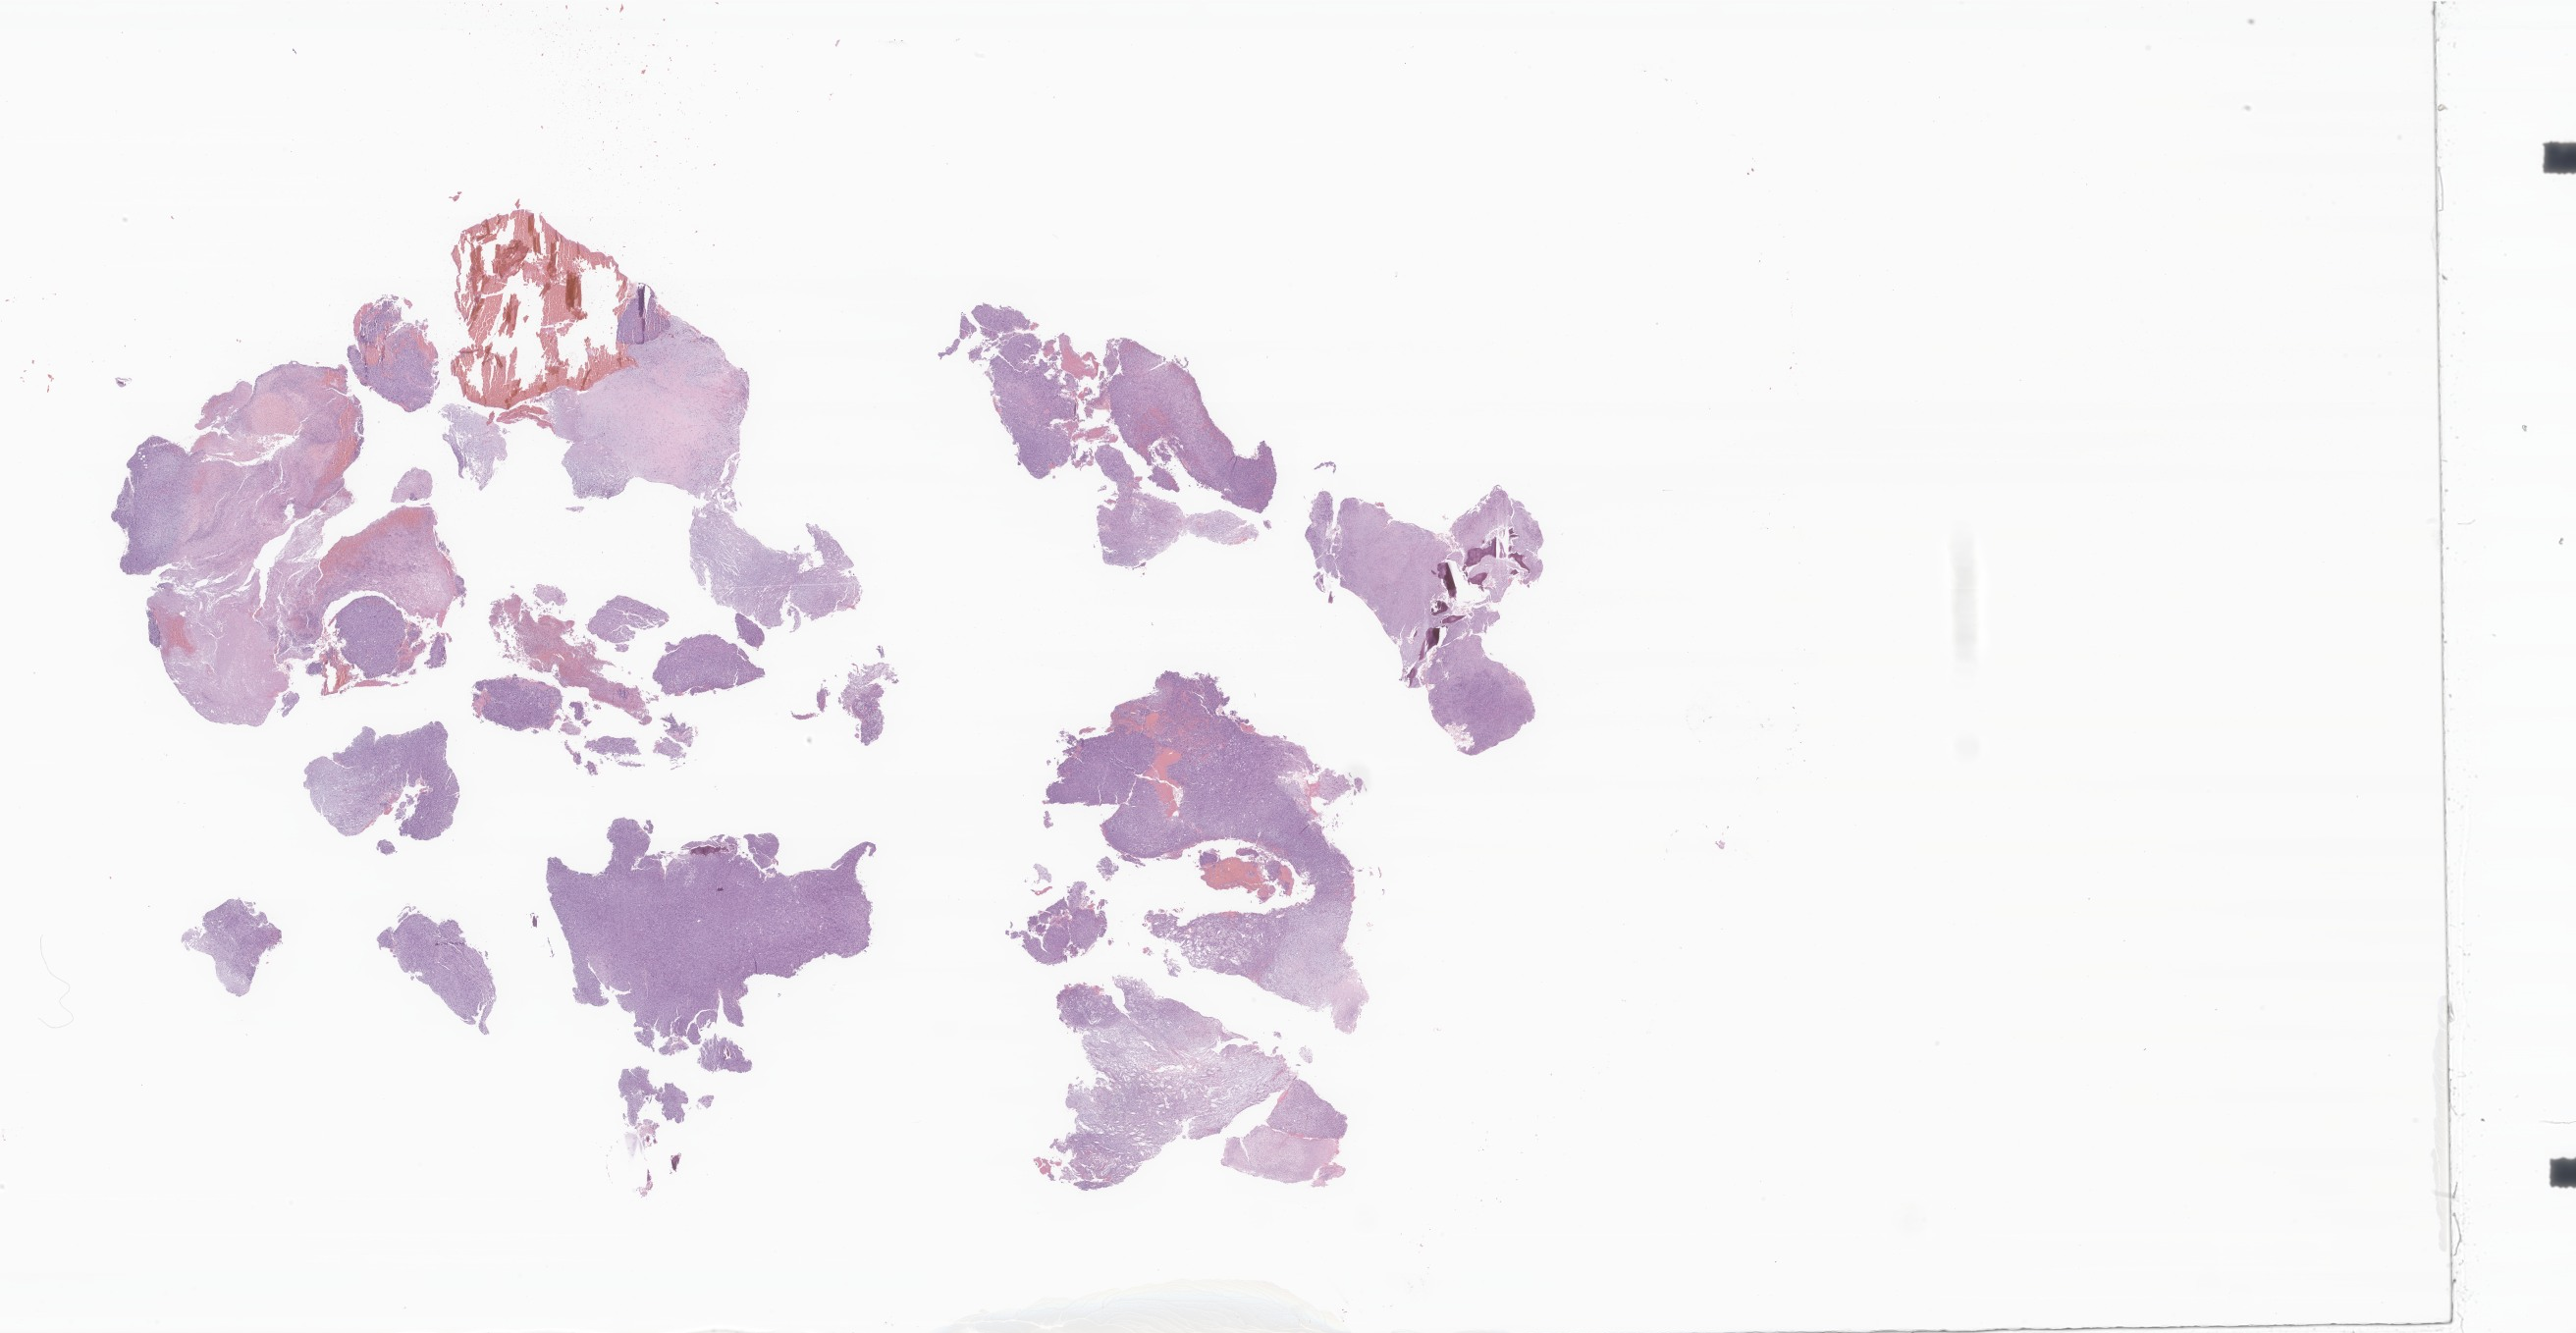
Haematoxylin and eosin whole-slide image of tumor tissue from the long bone of lower limb, low-resolution overview of the scanned area, about 44.3 x 22.9 mm; FFPE section. Patient: female, age 208 months (17 years 4 months).
Tissue or organ of origin (case record): long bones of lower limb and associated joints. Diagnosis (ICD-O-3 morphology term): Pleomorphic liposarcoma.